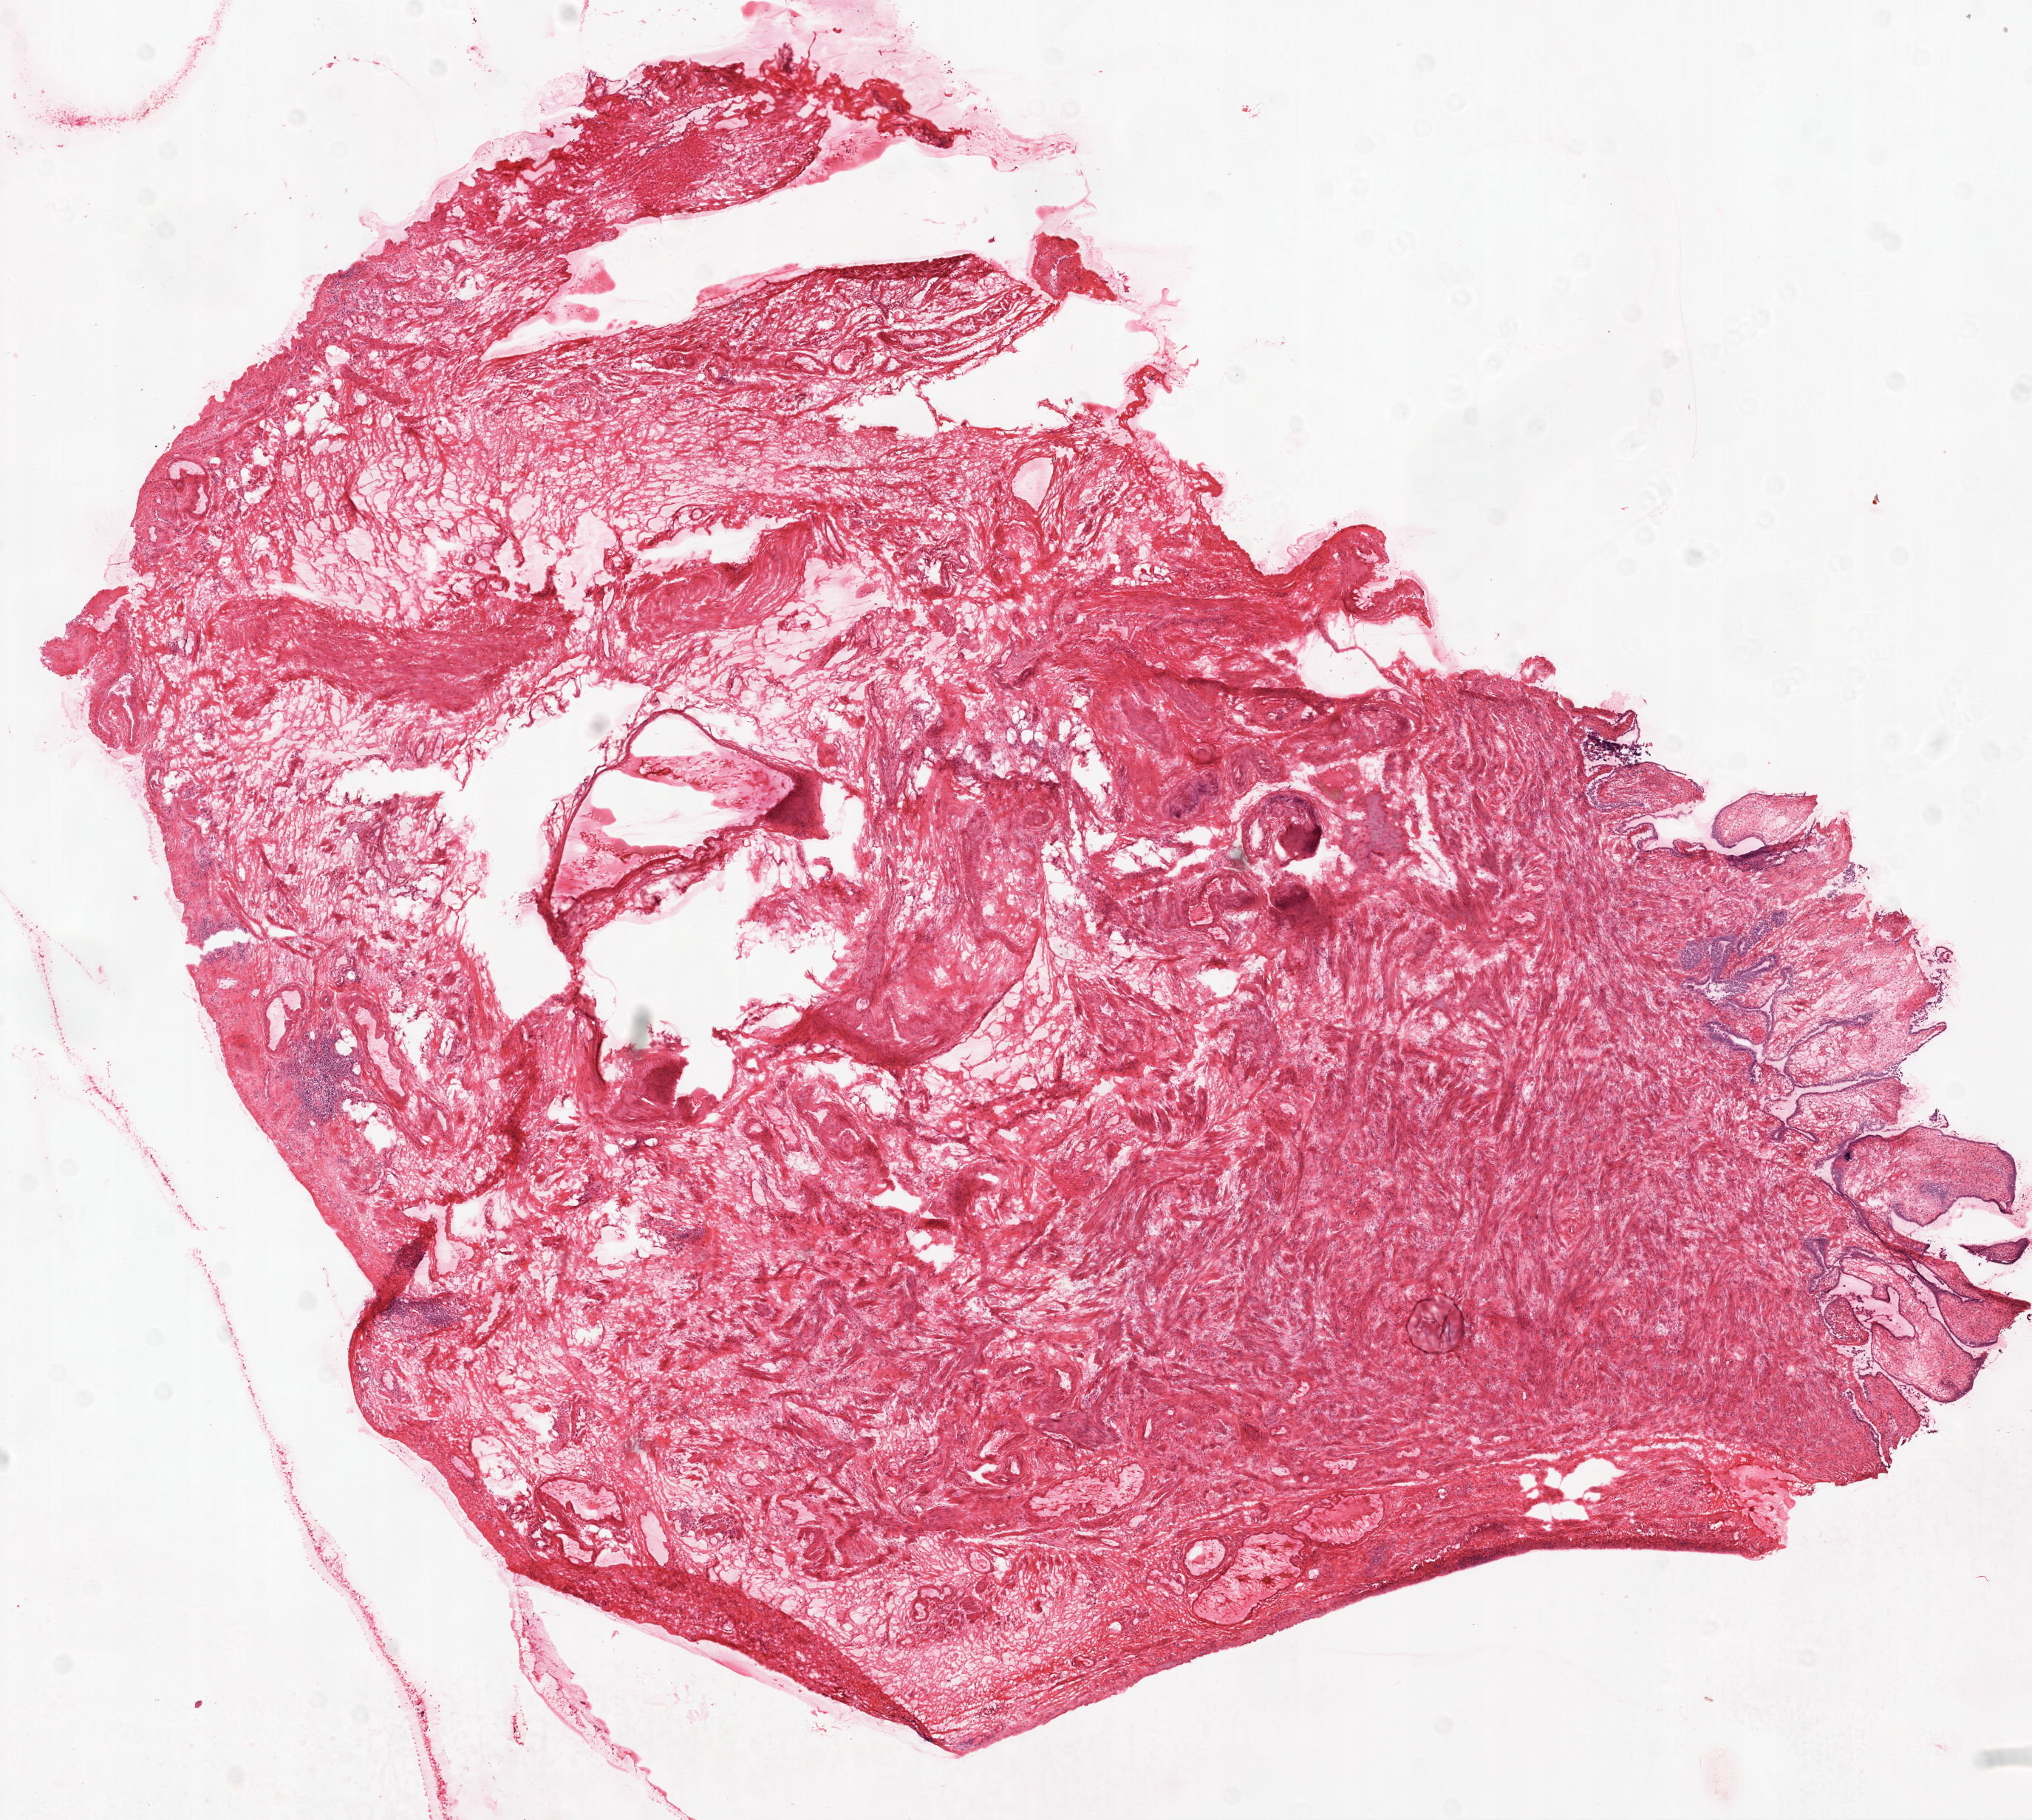
Digitized H&E tissue section (whole slide), a low-resolution overview of the entire scanned area, about 11.0 x 9.9 mm (slide scanned at 20x); frozen section; sample: solid tissue normal (non-tumour tissue), ovary. Female patient.
* this section: solid tissue normal (non-tumour) sample from the same patient
* patient diagnosis: Serous cystadenocarcinoma, NOS